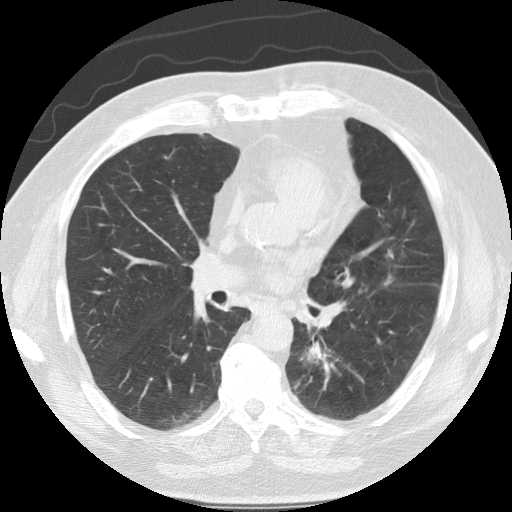
Chest CT (low-dose screening protocol), one axial image. First (baseline) screen. Lung window (W 1500 / L -600 HU). Standard (soft-tissue) reconstruction kernel (STANDARD). 512 × 512 image matrix, field of view 360 × 360 mm. Male, age 68 years at enrolment. Former smoker at enrolment.
• Lesion marked by an expert reader, bounding box <277,316,353,397> (left, top, right, bottom; pixels).
• The screening reader recorded 3 non-calcified nodules or masses ≥4 mm on this exam (left lower lobe, lingula, right lower lobe); which of them this box marks is not recorded.
• Official screen result: positive, change unspecified: nodule(s) >= 4 mm or enlarging nodule(s), mass(es), or other non-specific abnormalities suspicious for lung cancer.
• Later outcome: lung cancer diagnosed 35 days after this screen — squamous cell carcinoma, NOS, left lower lobe, poorly differentiated (G3), stage IIB (AJCC 6th edition), 40 mm at pathology.